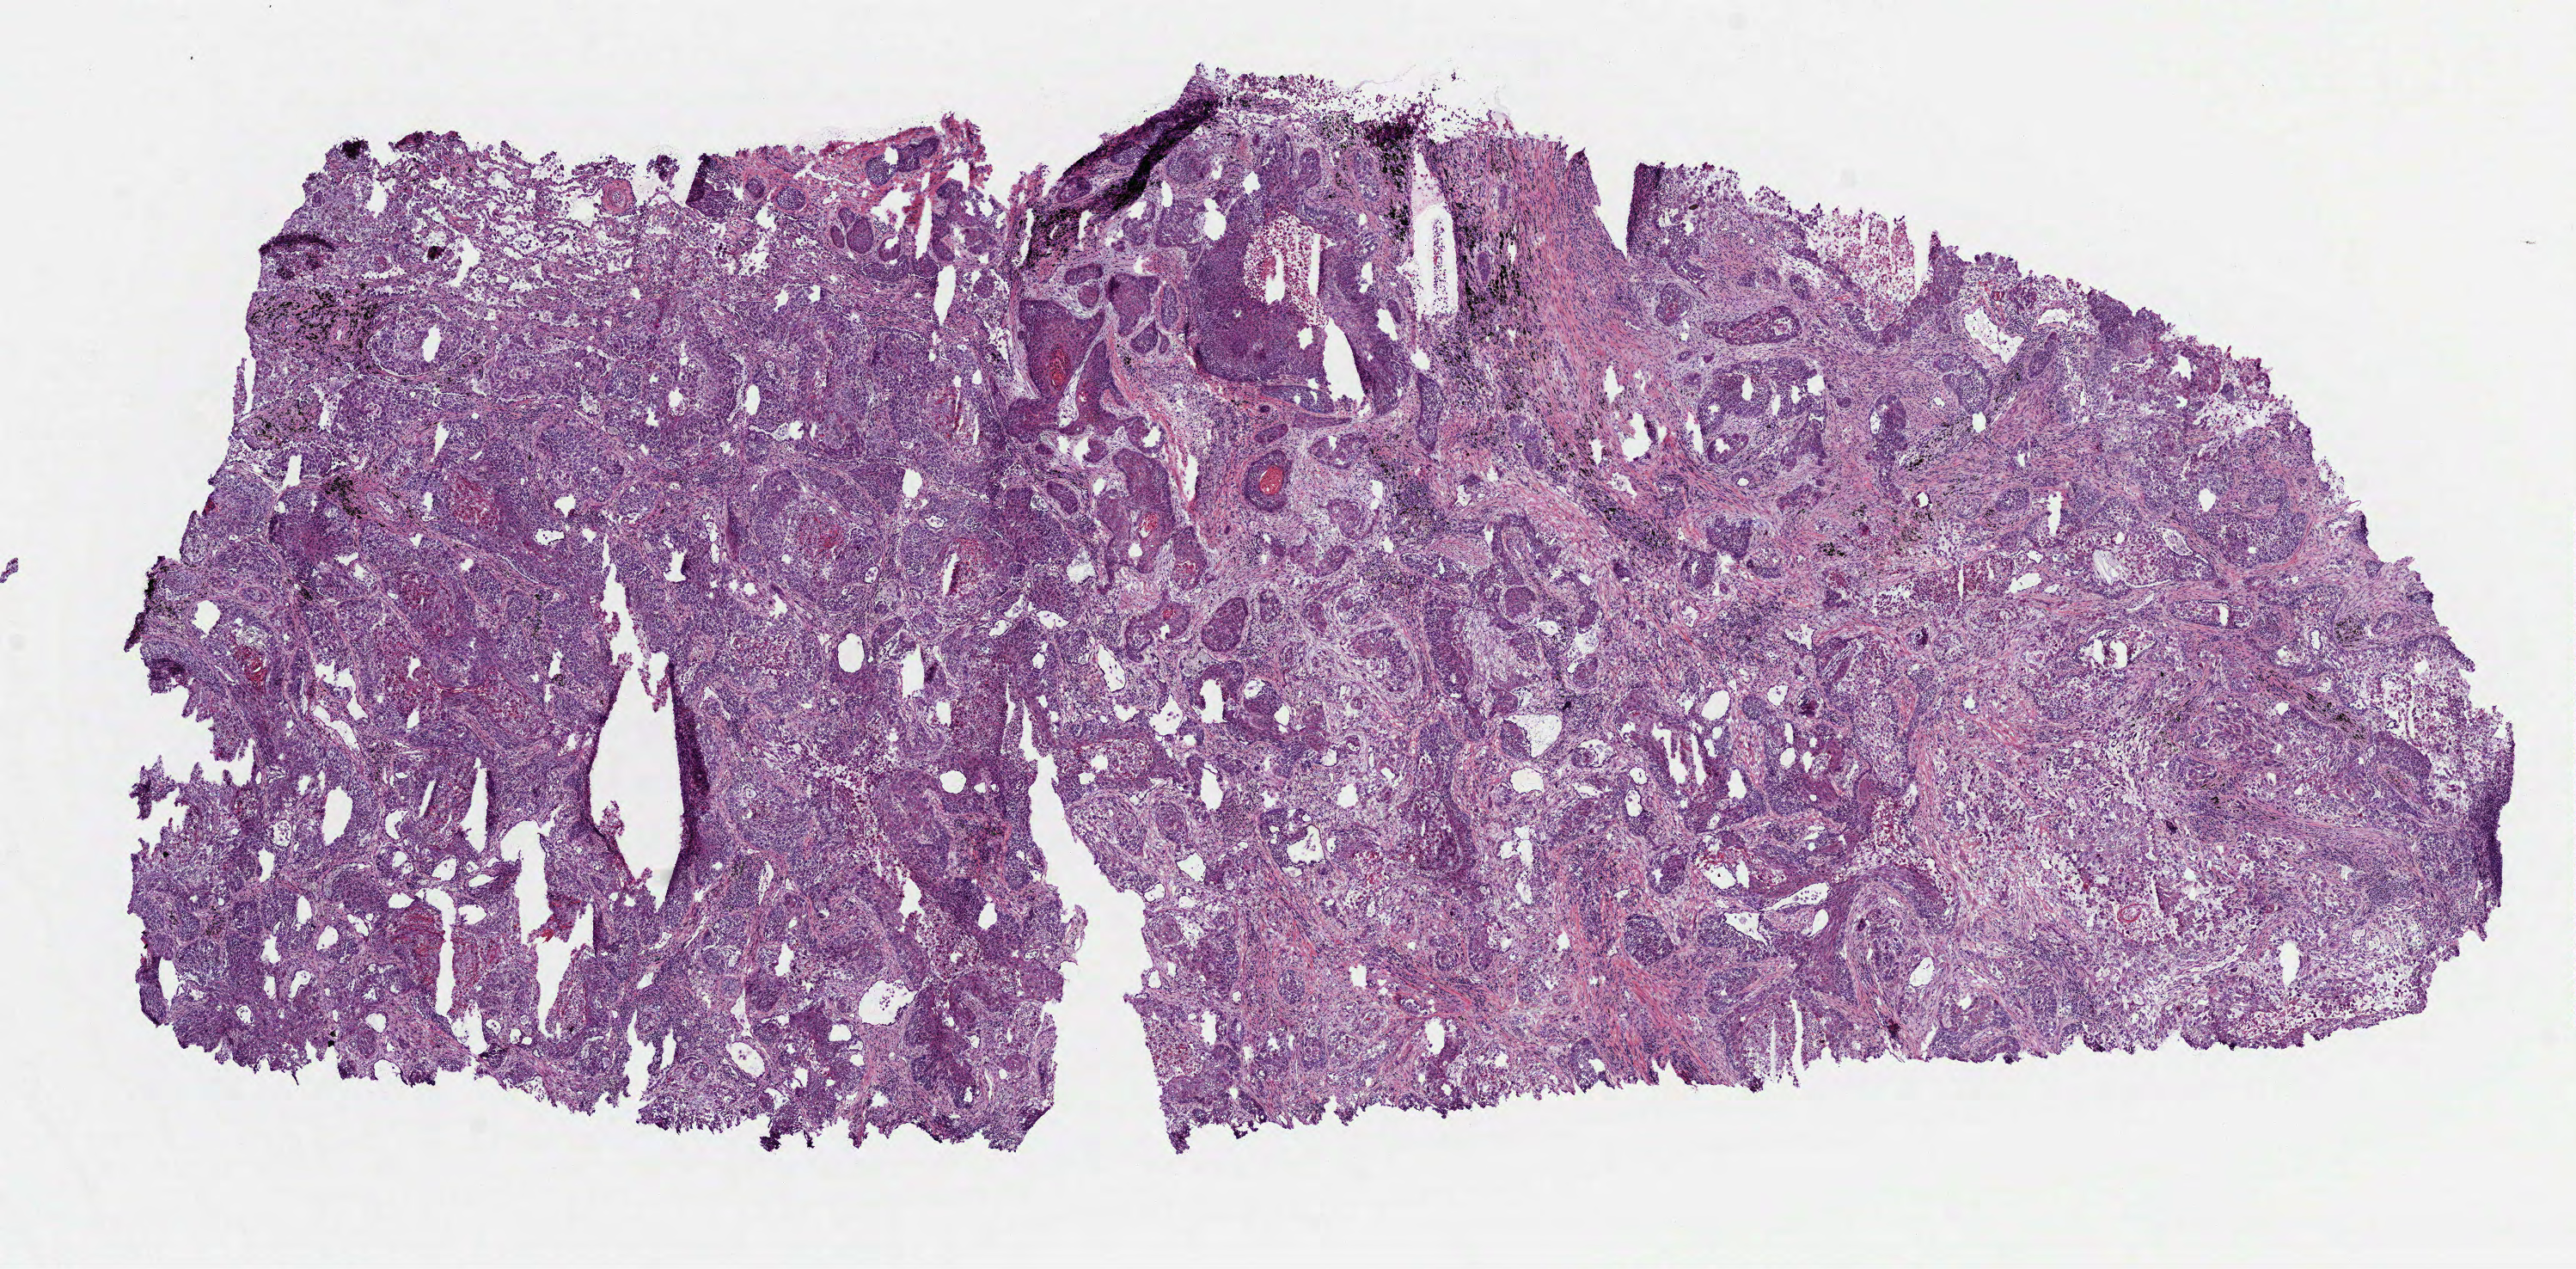
Whole-slide histology image, H&E — shown as a low-resolution overview of the whole scanned area (about 12.1 x 6.0 mm, from a 40x scan). Frozen section. Sample: primary tumour, lung. Male patient; age at initial diagnosis 64 years. Pathologist review of this section (percent, as recorded): tumour cells 98%, tumour nuclei 70%, normal cells 0%, stromal cells 0%, necrosis 2%. Inflammatory infiltration, as recorded: lymphocyte infiltration 15%, monocyte infiltration 0%, neutrophil infiltration 2%.
- AJCC pathologic stage: IB (6th edition)
- laterality: right
- histologic diagnosis: Squamous cell carcinoma, NOS (upper lobe, lung)